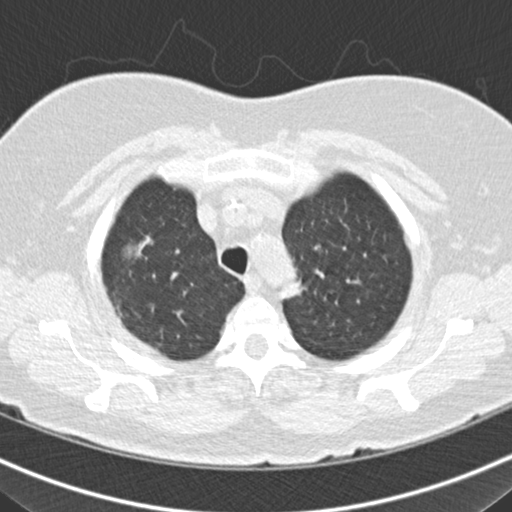
Low-dose screening chest CT, one axial slice. Position 139 of 160 along the scan axis. Reconstruction kernel B30f. 120 kVp. Lung window (W 1500 / L -600 HU). 2 mm slice thickness. 512 × 512 image matrix.
Annotated regions visible in this slice (expert manual segmentation):
- lesion 3 (nodule, upper lobe of right lung): box from (x=132, y=239) to (x=147, y=258) px